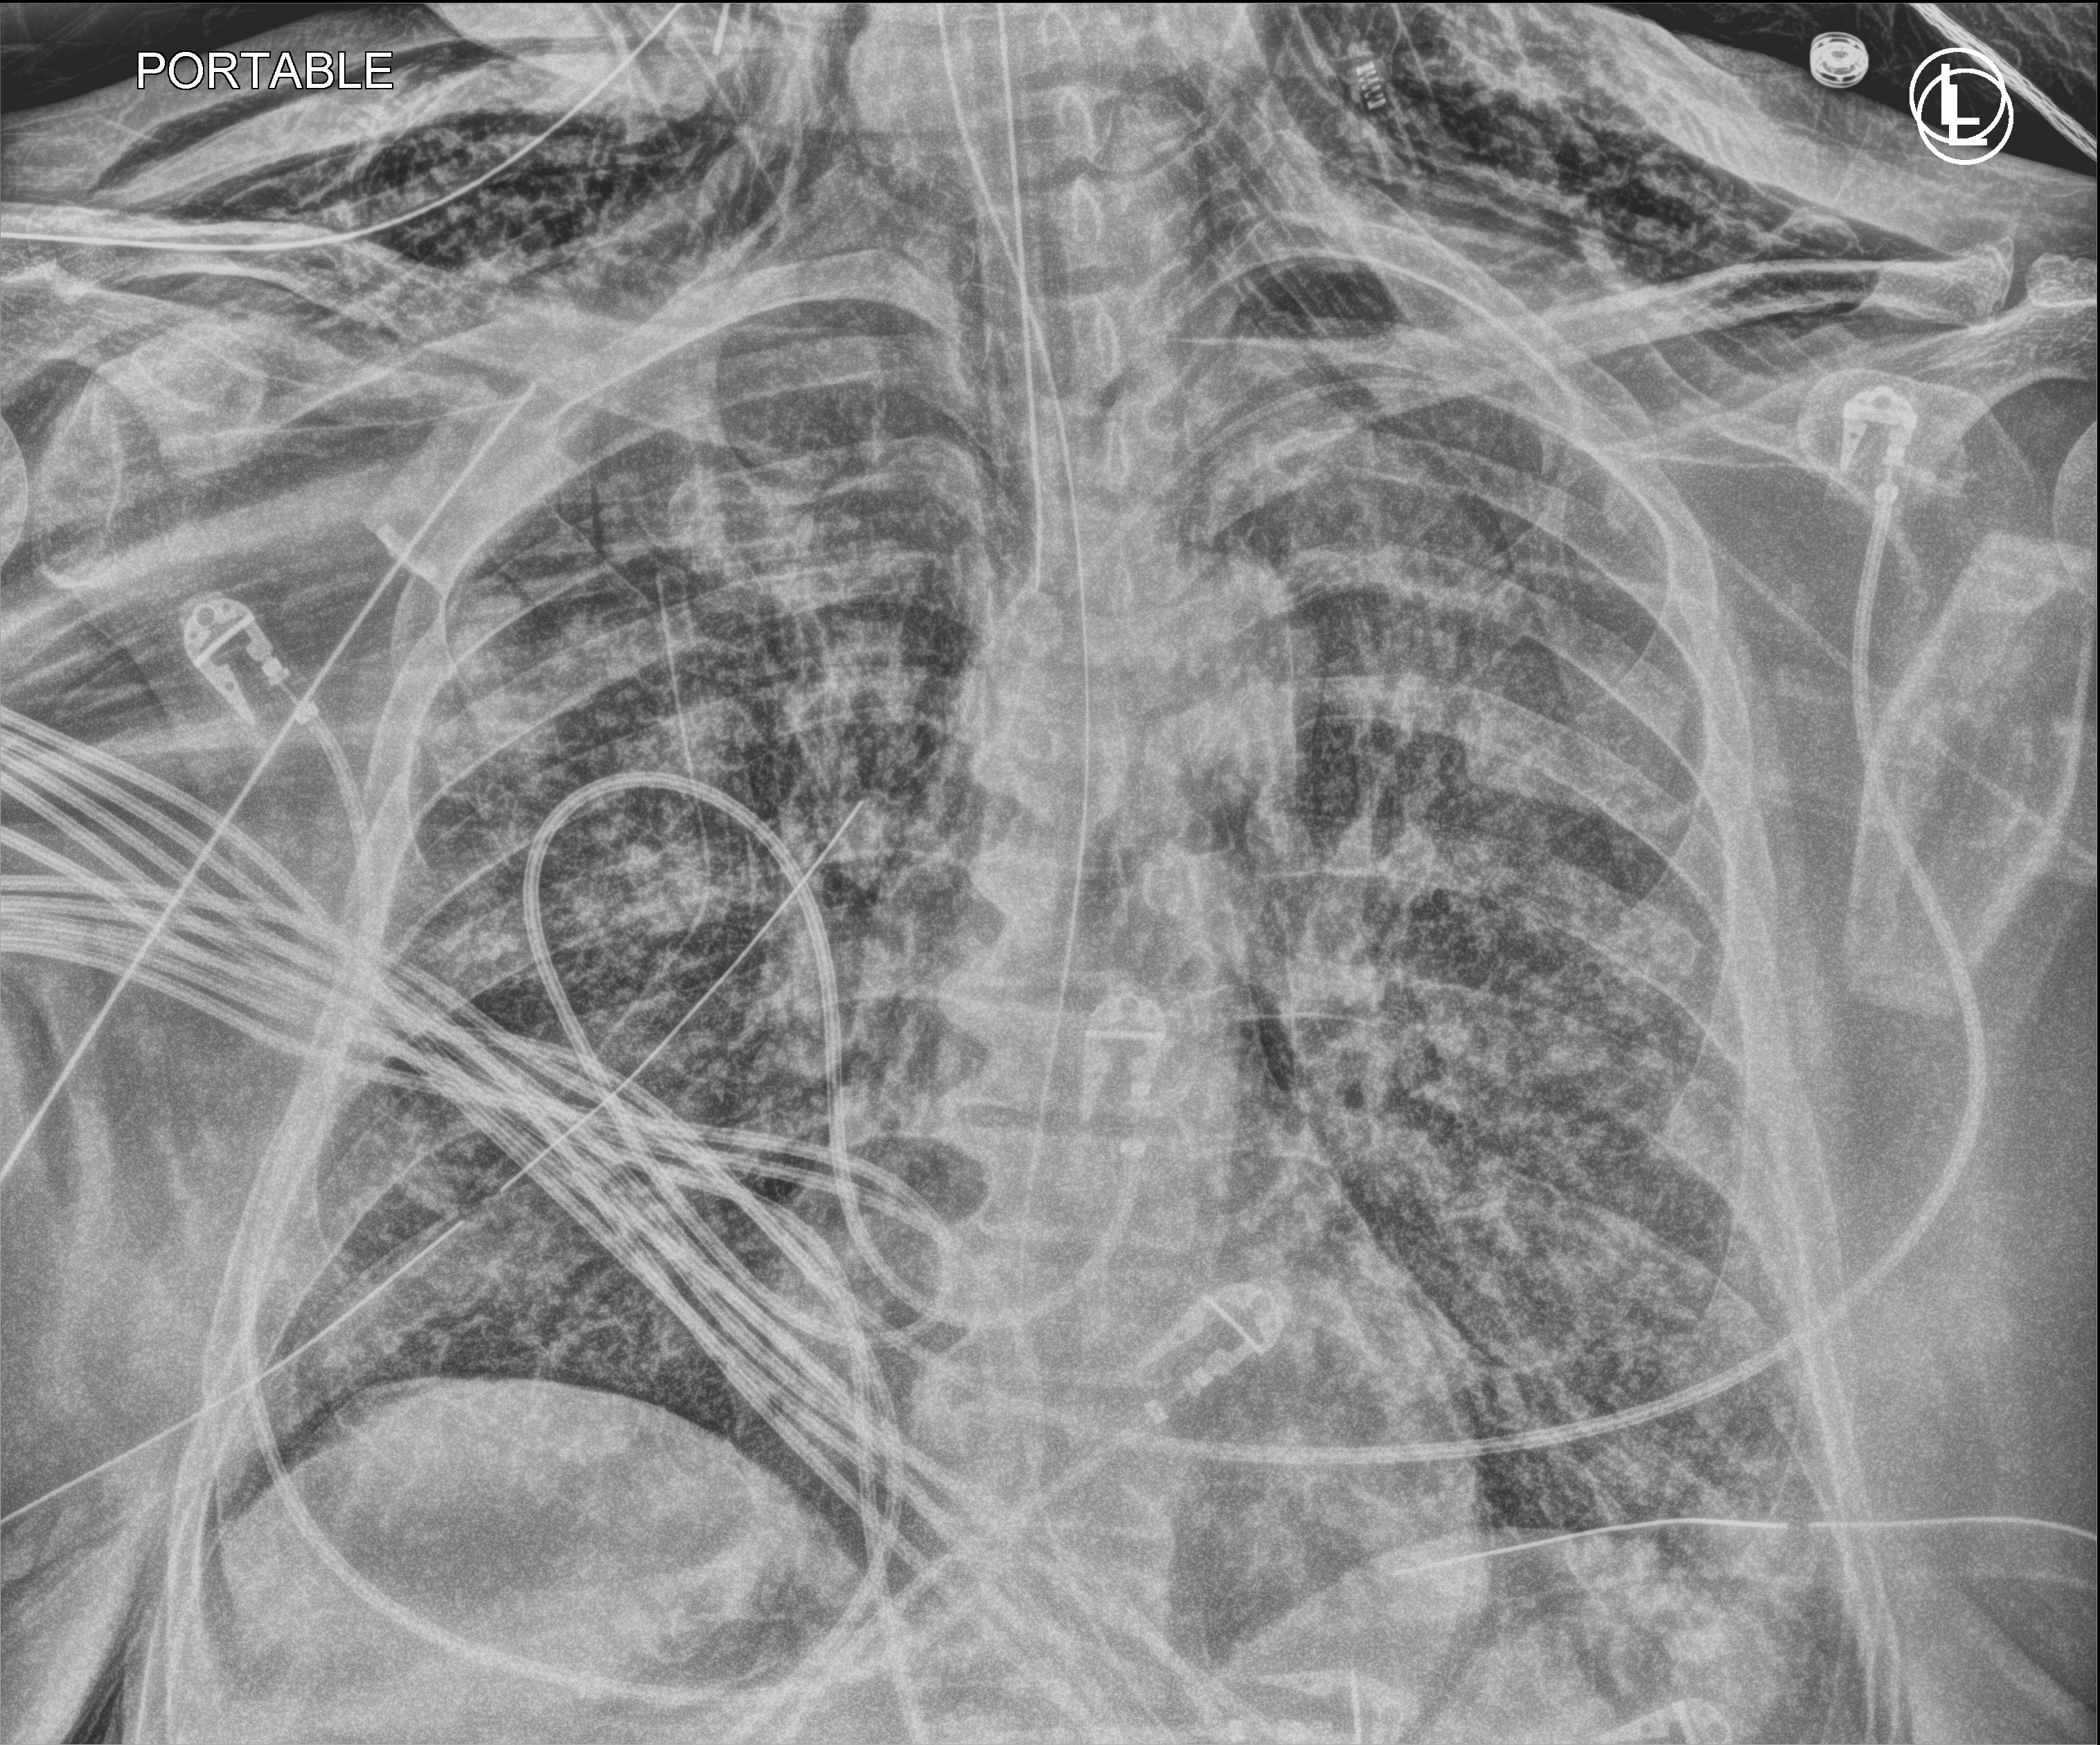
Portable chest radiograph; anteroposterior (AP) projection. Adult patient hospitalised with COVID-19, age 18–59 years.
From the hospital-stay record, not from the radiograph (when in the stay this image was taken is not recorded): COPD (admission record): no; admitted to intensive care during this hospital stay: yes; mechanically ventilated during this hospital stay: yes.